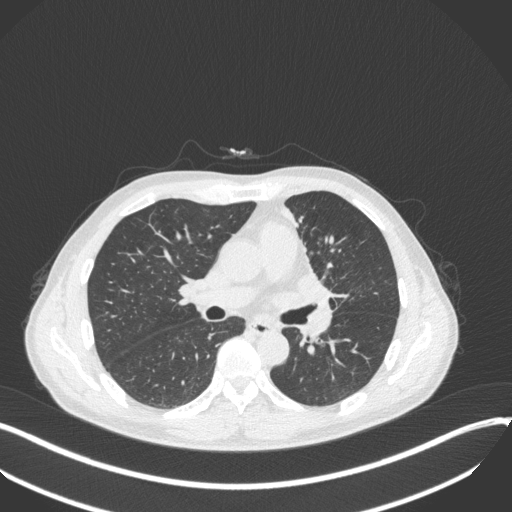
Chest CT, one axial slice. Position 186 of 411 along the scan axis. Reconstruction kernel B31f. 120 kVp. Lung window (W 1500 / L -600 HU). 512 × 512 image matrix, field of view 400 × 400 mm. Male patient, age 56 years. From the clinical record (not read from this slice): clinical TNM (as recorded): T2a N0 M0.
Annotated regions visible in this slice (bounding box drawn by a radiologist):
- lung tumour (recorded histology: squamous cell carcinoma): bounding box [x1, y1, x2, y2] px = [265, 264, 331, 306]